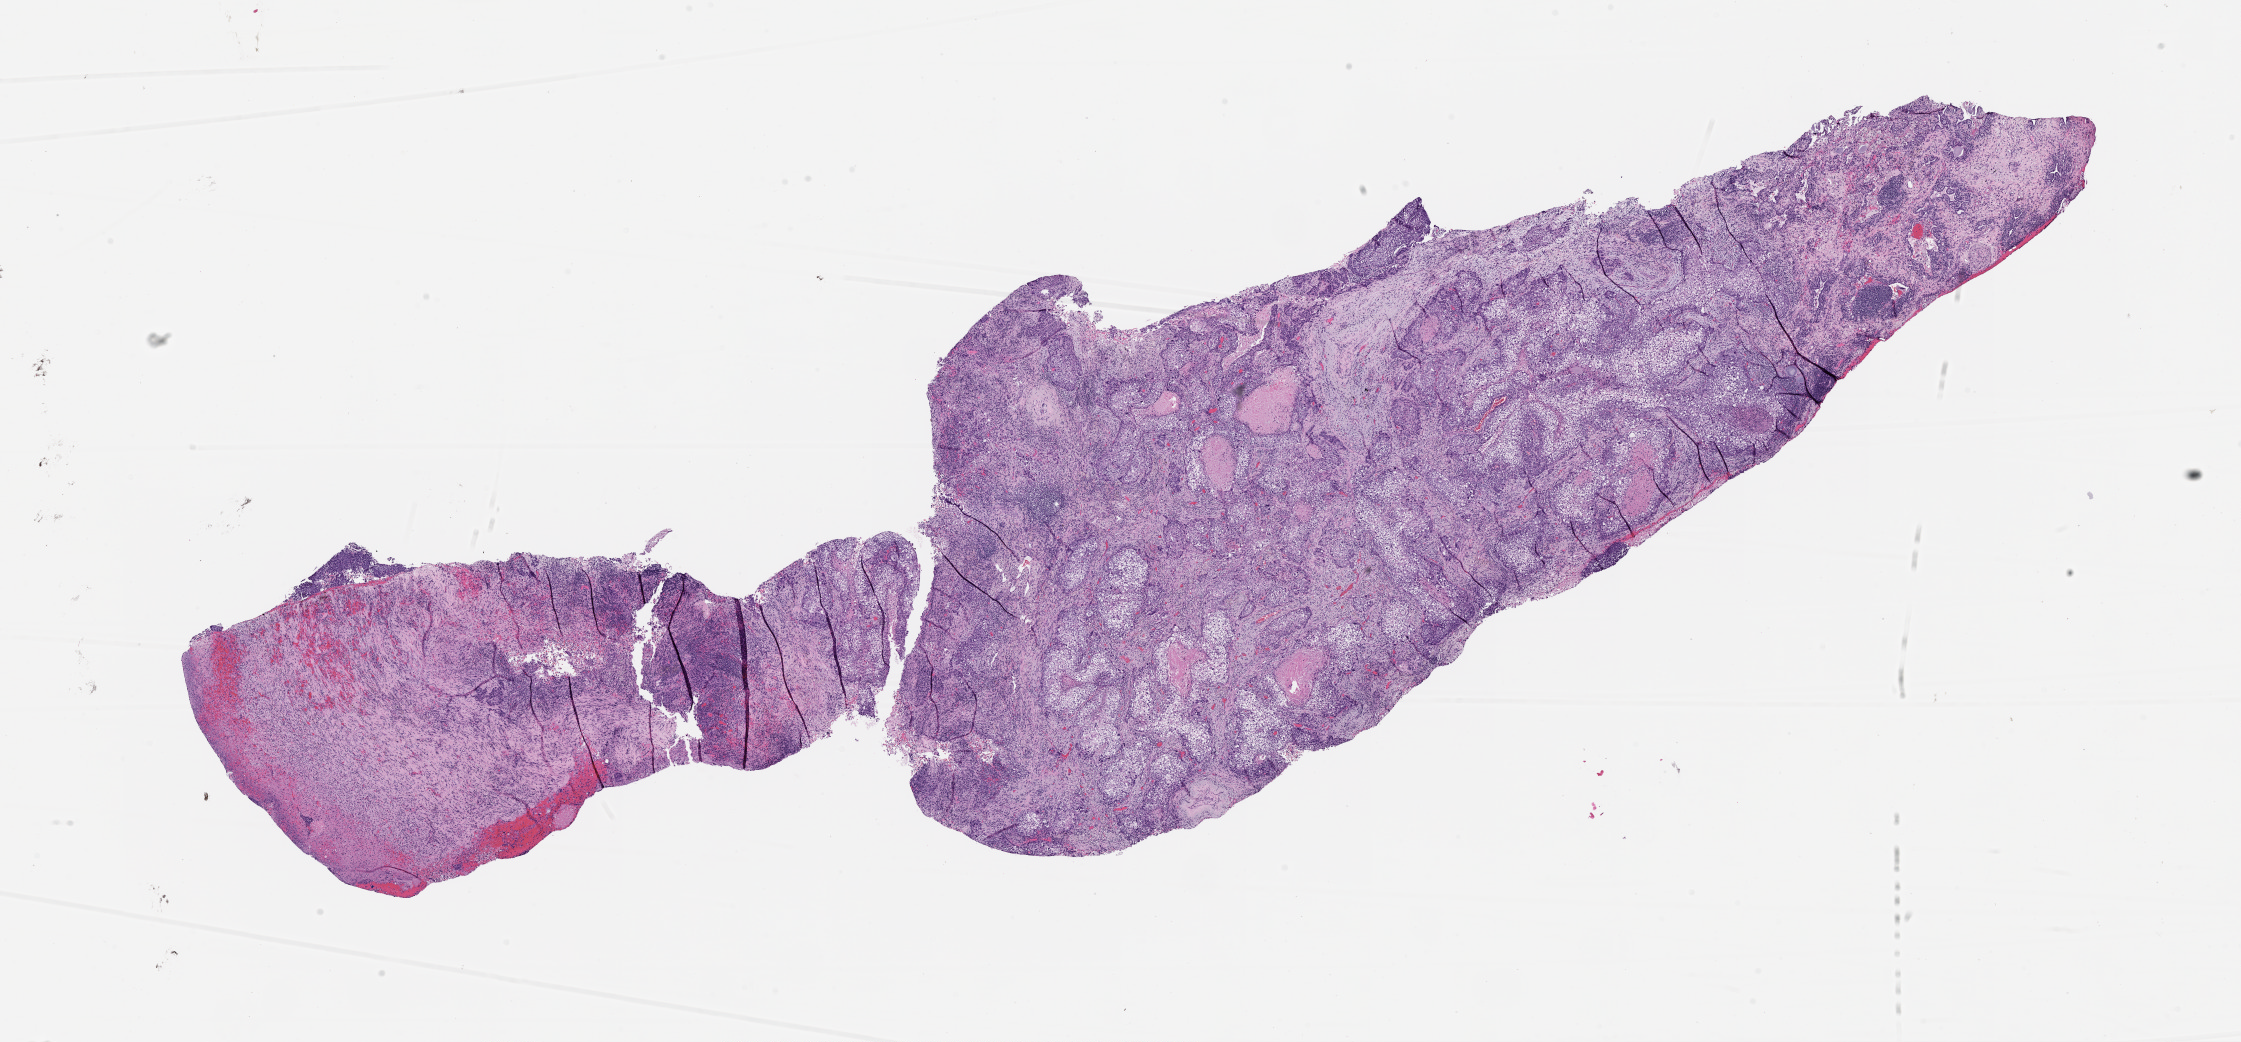
Digitized H&E-stained tissue section (whole slide) — a low-resolution overview of the entire scanned area, about 18.0 x 8.4 mm; lung, tumour tissue. 82-year-old female patient.
Patient diagnosis (cohort enrolment): squamous cell carcinoma (lung).